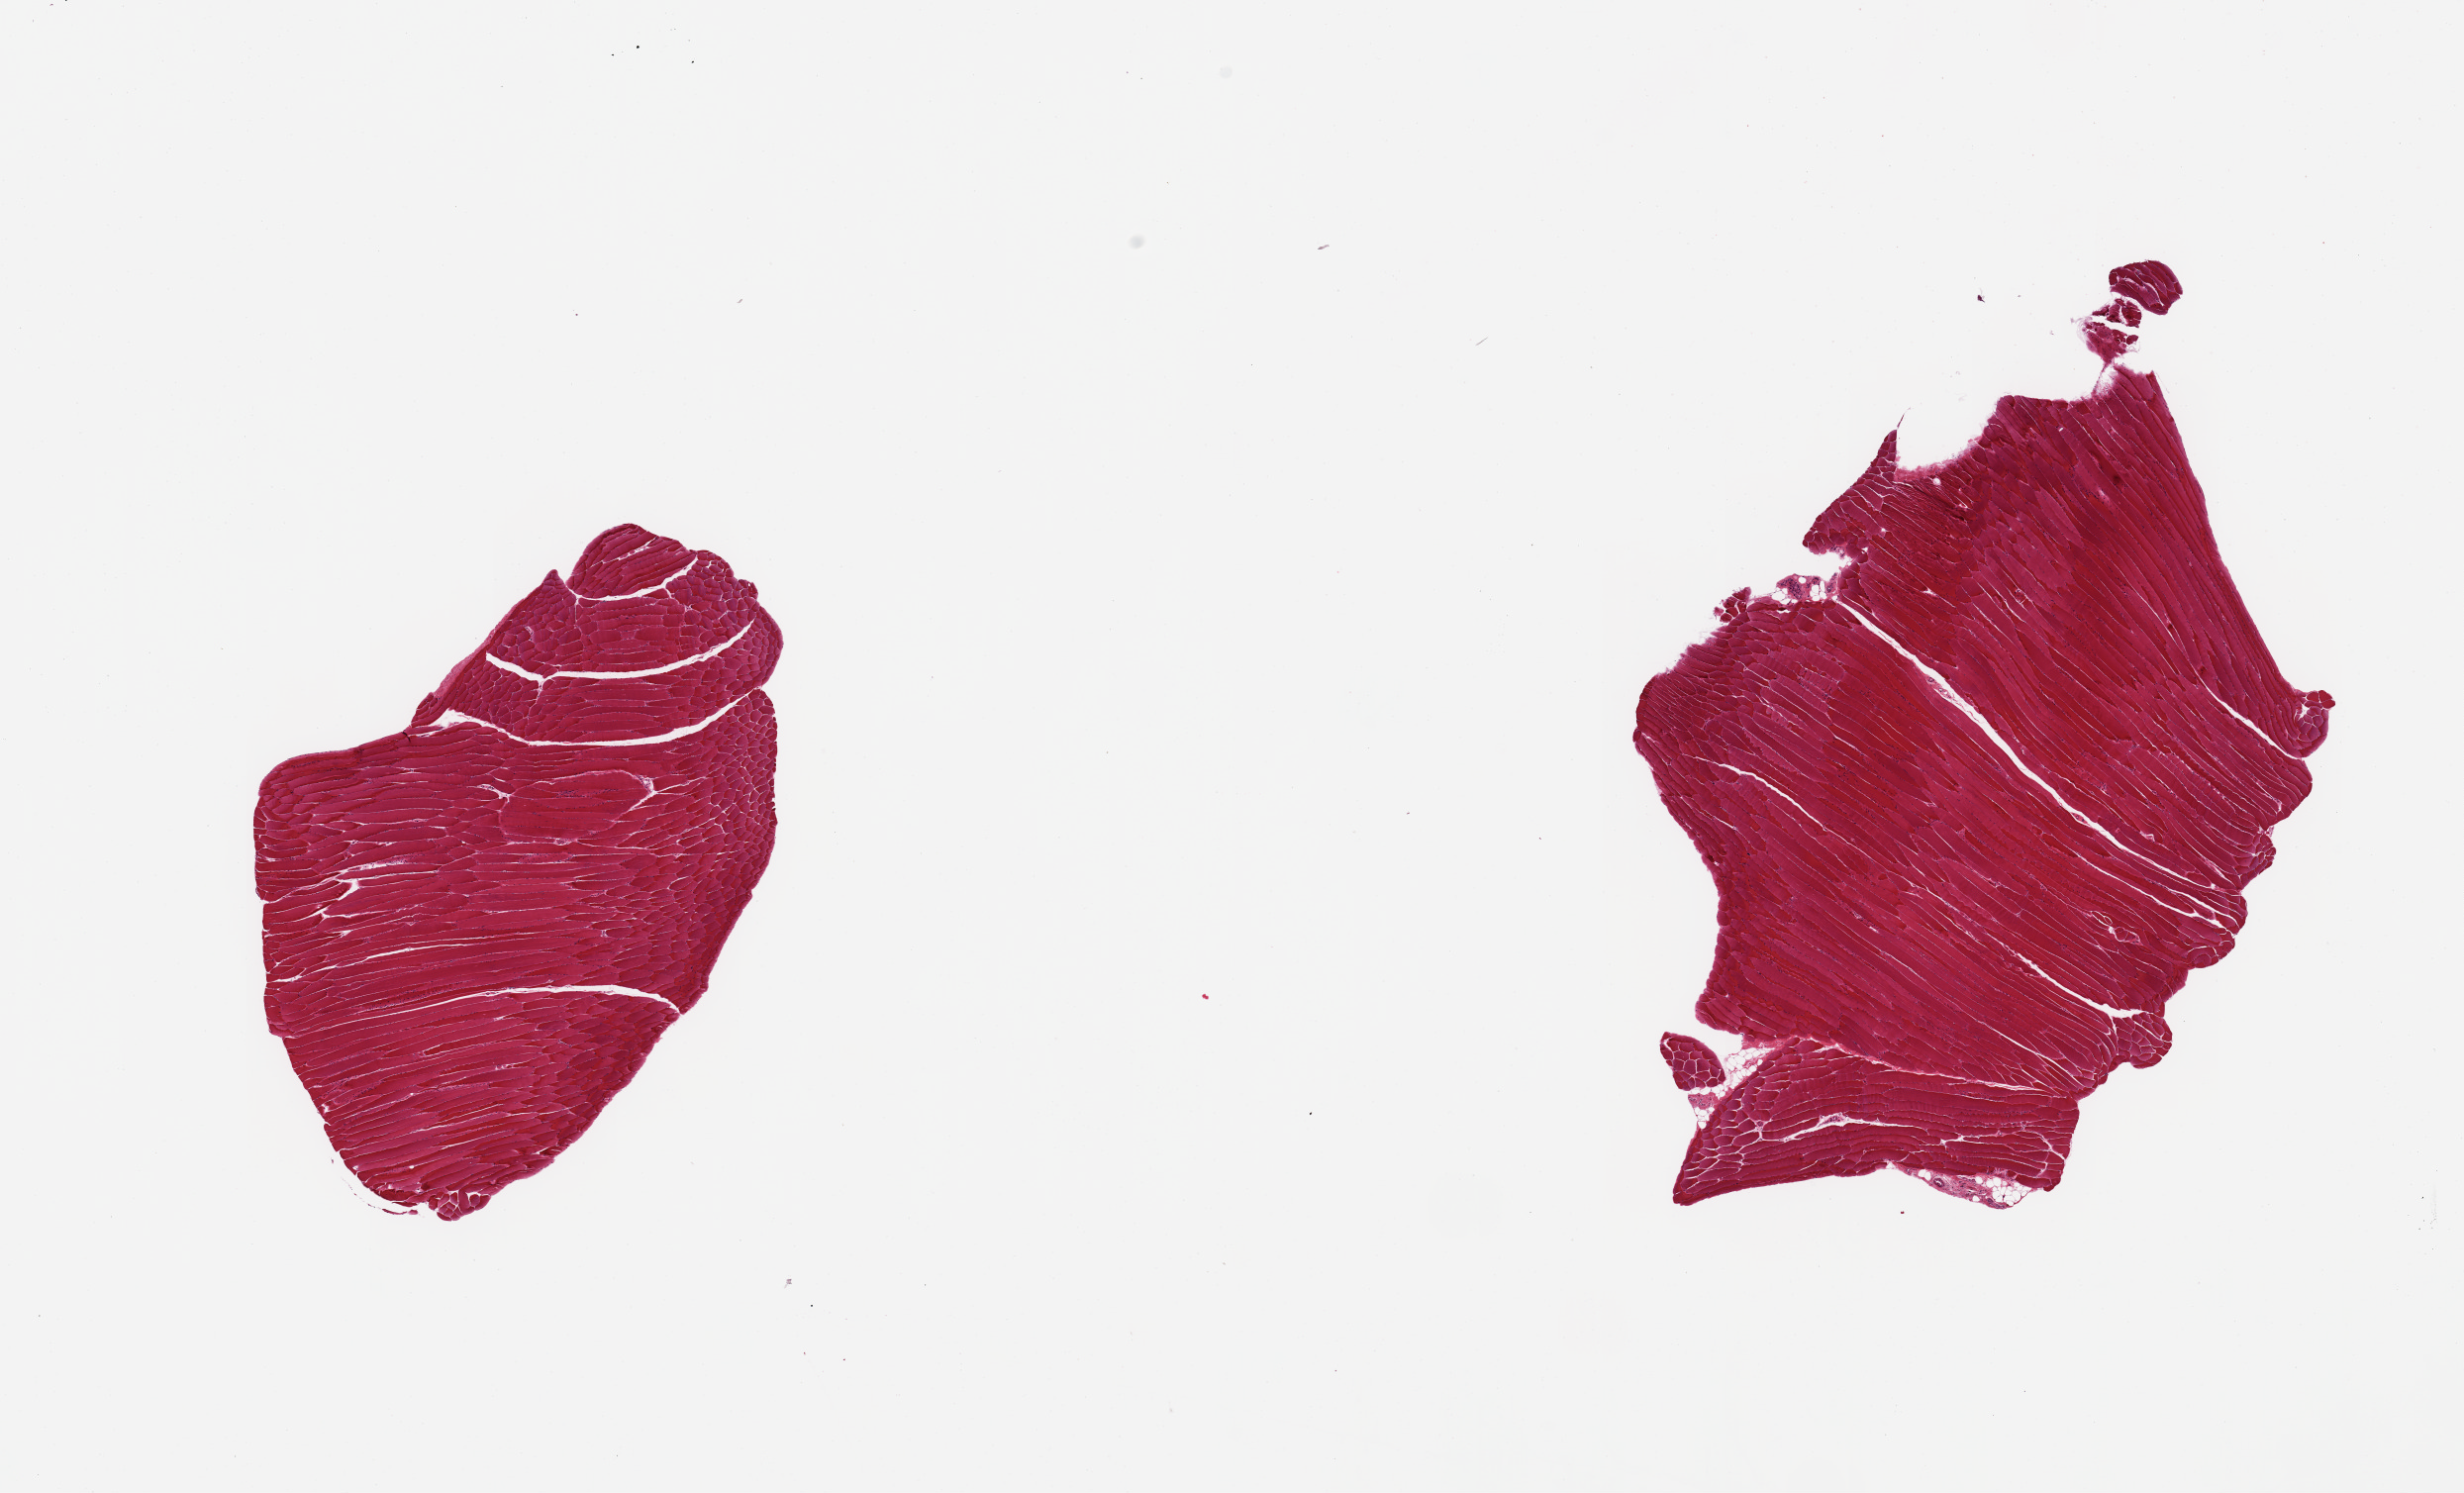
Digitized haematoxylin and eosin-stained section, a low-resolution overview of the entire scanned area, about 19.7 x 11.9 mm (slide scanned at 20x). PAXgene-fixed paraffin-embedded (PFPE) section. Section of skeletal muscle (target tissue). Donor tissue sample. Donor sex: male.
Review note (as recorded): 2 pieces; well trimmed skeletal muscle.